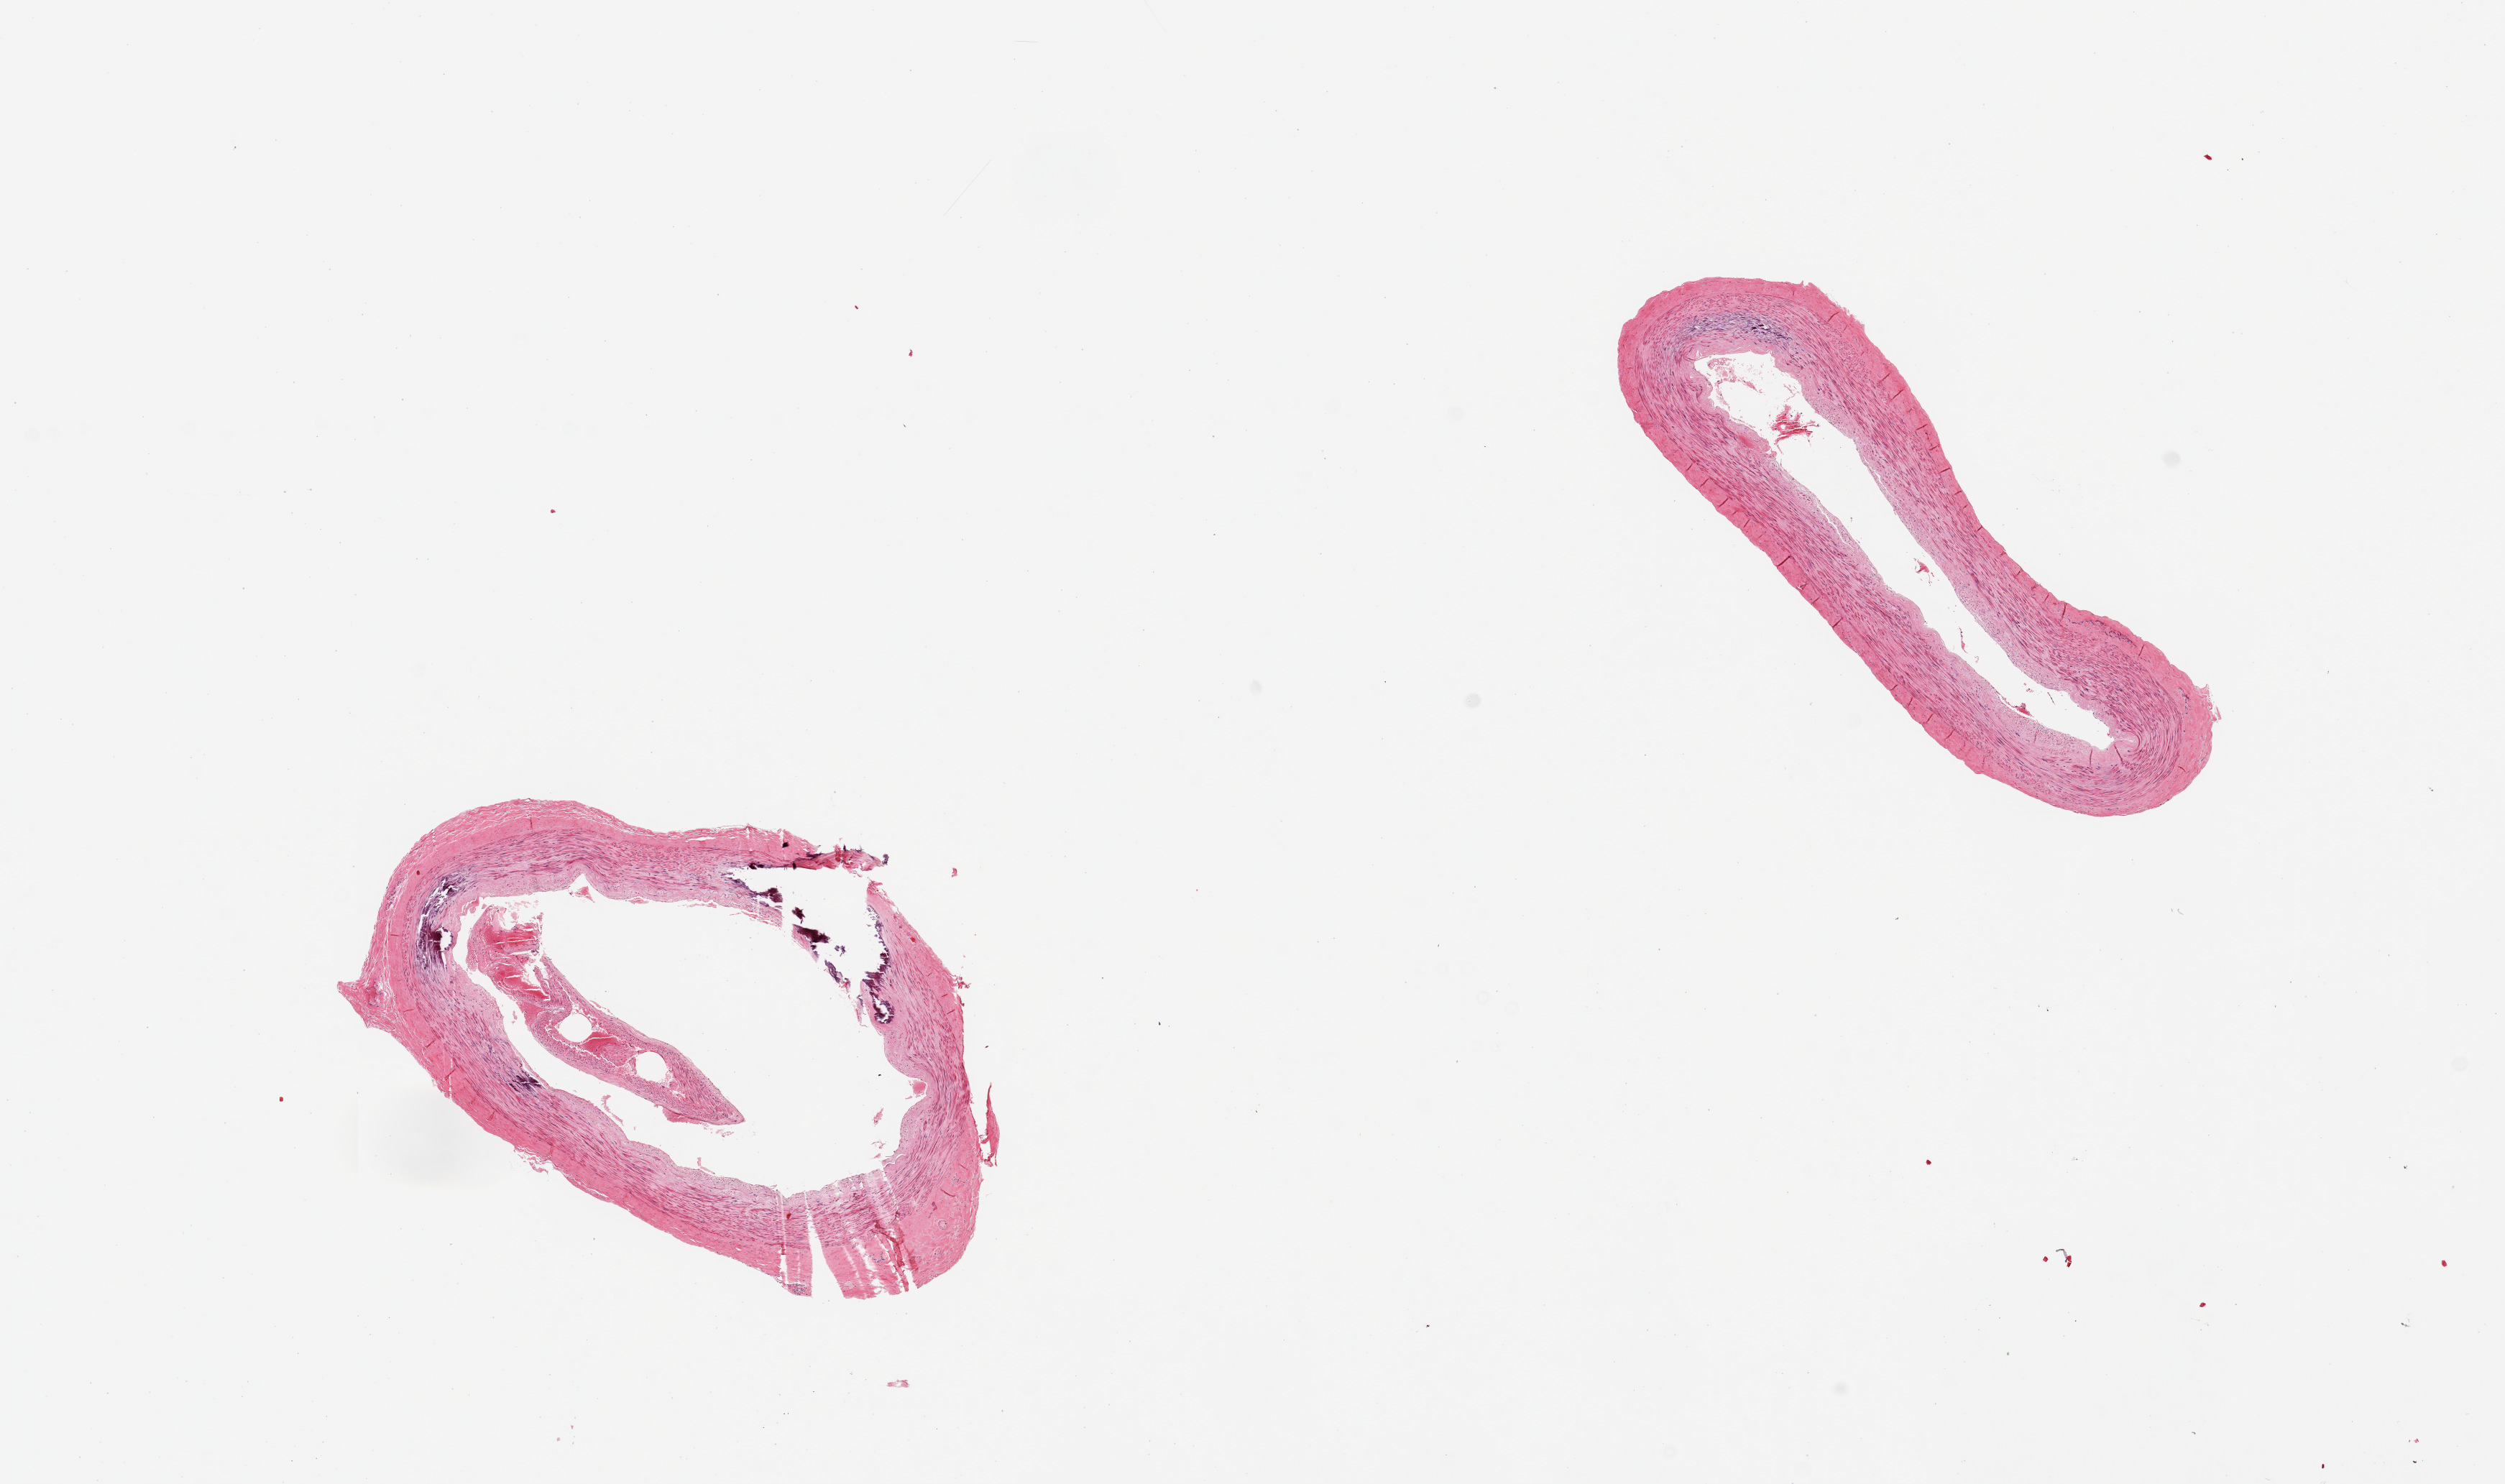
Haematoxylin and eosin whole-slide image, brightfield, a low-resolution overview of the entire scanned area, about 13.8 x 8.2 mm (acquisition: 20x scan); PAXgene-fixed, paraffin-embedded tissue; section of tibial artery (target tissue); tissue donor sample. Donor: male.
Review note (as recorded): 2 pieces; 1 with large calcified deposit; well trimmed.